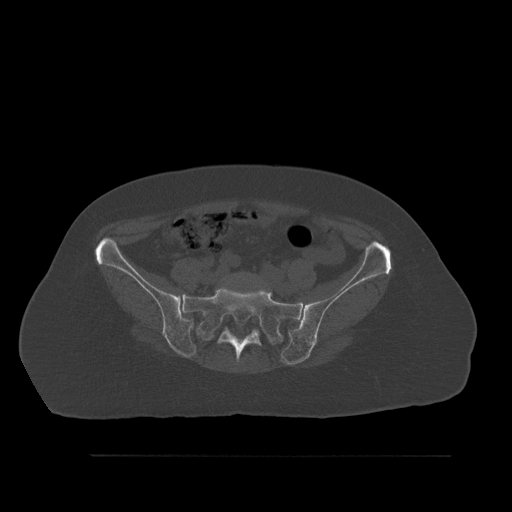
CT including the spine, one axial slice; position 172 of 527 along the scan axis; bone window (W 1800 / L 400 HU); 512 × 512 image matrix, field of view 470 × 470 mm. Patient: female, 73 years. Case-level facts recorded for this patient, not image findings: primary cancer: breast; vertebrae with lytic lesions (as recorded): L2.
Structures marked on this image (semi-automatically segmented with operator editing):
- L5 vertebra: bounding box <246,274,249,276> (left, top, right, bottom; pixels)